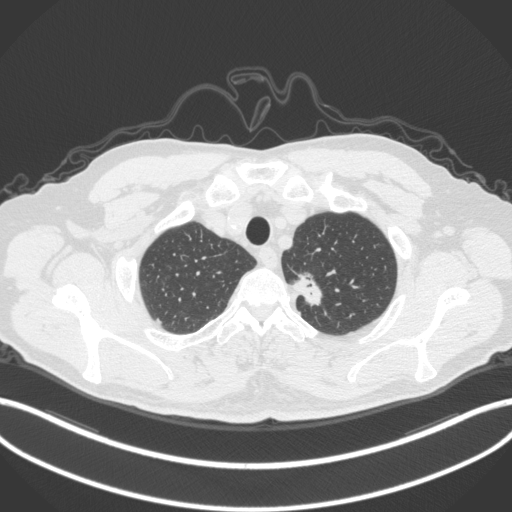
Chest CT, one axial slice. Position 332 of 382 along the scan axis. Reconstruction kernel B31f. Lung window (W 1500 / L -600 HU). 512 × 512 image matrix. Patient: male, 64 years. Case-level facts recorded for this patient, not image findings: clinical TNM (as recorded): T1c N0 M0.
Annotated regions visible in this slice (bounding box drawn by a radiologist):
- lung tumour (recorded histology: adenocarcinoma): bounding box (x1, y1, x2, y2) in pixels: (290, 267, 327, 311)